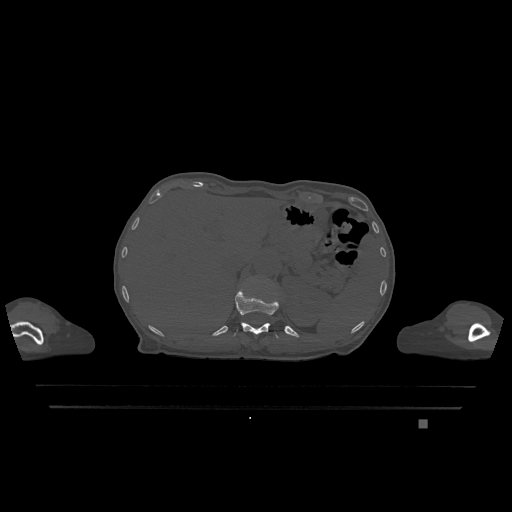
CT including the spine, one axial slice; position 527 of 1317 along the scan axis; bone window (W 1800 / L 400 HU); 0.5 mm slice thickness; 512 × 512 image matrix. Female patient, age 74 years. From the clinical record (not read from this slice): primary cancer: lung; vertebrae with lytic lesions (as recorded): T1, T4, T5, T6, L4, L5.
Annotated regions visible in this slice (semi-automatically segmented with operator editing):
- T12 vertebra: bounding box <233,287,279,338> (left, top, right, bottom; pixels)